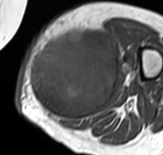
MRI of an extremity soft-tissue mass, one axial slice. Slice 29 of 65 in the series (ordered by position). MR volume resampled by the dataset authors to the PET/CT grid (not the native acquisition matrix). 3.27 mm slice thickness. 163 × 155 image matrix, field of view 159 × 151 mm. Female patient. Case-level facts recorded for this patient, not image findings: histological type: pleomorphic leiomyosarcoma; grade: high; site of the primary tumour: left thigh.
Structures marked on this image (expert contour drawn on MRI and transferred to this co-registered scan by the dataset authors):
- gross tumour volume including surrounding oedema: bounding box [x1, y1, x2, y2] px = [28, 31, 120, 121]
- gross tumour volume (mass): [28, 31, 118, 121]